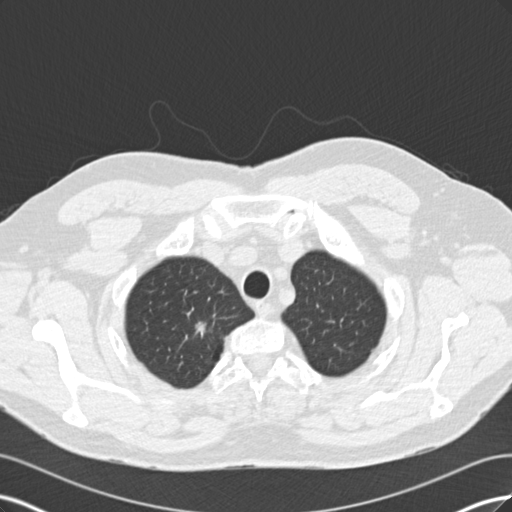
Axial slice from a low-dose chest CT screening exam, first (baseline) screen, lung window (W 1500 / L -600 HU), 2 mm slice thickness, slice 21 of 171 in the series. Male, age 56 years at enrolment. Former smoker at enrolment.
- Expert reader's lesion annotation, box from (x=175, y=309) to (x=224, y=353) px.
- The exam's reader record, not a measurement of the box and not confirmed to be the same lesion: non-calcified nodule or mass ≥4 mm, right upper lobe, 14 × 8 mm, spiculated (stellate) margins.
- Participant outcome: lung cancer diagnosed 146 days after this screen — adenocarcinoma, NOS, right upper lobe, poorly differentiated (G3), stage IA (AJCC 6th edition), 12 mm at pathology.